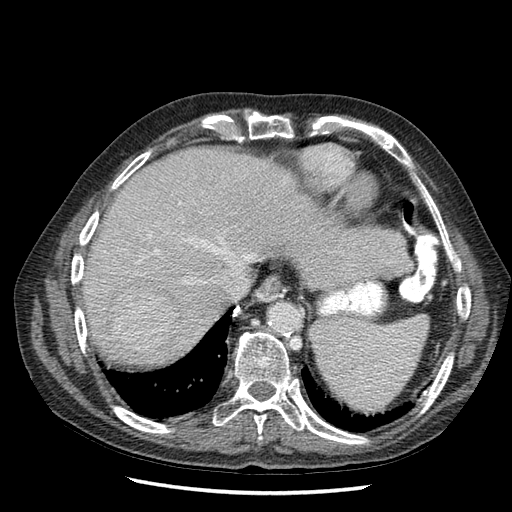
Contrast-enhanced abdominal CT (liver protocol), one axial slice. Position 51 of 67 along the scan axis. Reconstruction kernel STANDARD. 120 kVp. Soft-tissue window (W 400 / L 40 HU). 2.5 mm slice thickness. 512 × 512 image matrix, field of view 360 × 360 mm. Case-level facts recorded for this patient, not image findings: diagnosis: hepatocellular carcinoma (patient treated with transarterial chemoembolisation; whether this scan precedes or follows treatment is not stated here); TNM stage (as recorded): Stage-I; Child-Pugh class: A.
Outlined on this slice (semi-automatic segmentation, software-assisted and operator-edited):
- liver parenchyma outside the tumour (the mass and vessels are separate outlines, so this box may not span the whole liver): bounding box [x1, y1, x2, y2] px = [82, 144, 412, 371]
- mass: [110, 287, 177, 351]
- liver vessels: [141, 250, 244, 293]